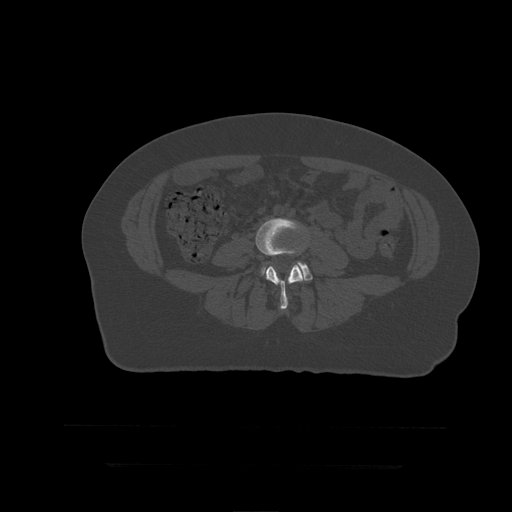
CT including the spine, one axial slice; slice 89 of 399 in the series (ordered by position); 120 kVp; bone window (W 1800 / L 400 HU); 1.25 mm slice thickness; 512 × 512 image matrix. Patient age 41 years. Case-level facts recorded for this patient, not image findings: primary cancer: breast.
Structures marked on this image (semi-automatic segmentation, software-assisted and operator-edited):
- L4 vertebra: box from (x=256, y=218) to (x=308, y=310) px
- L5 vertebra: (x=261, y=262)–(x=313, y=281)